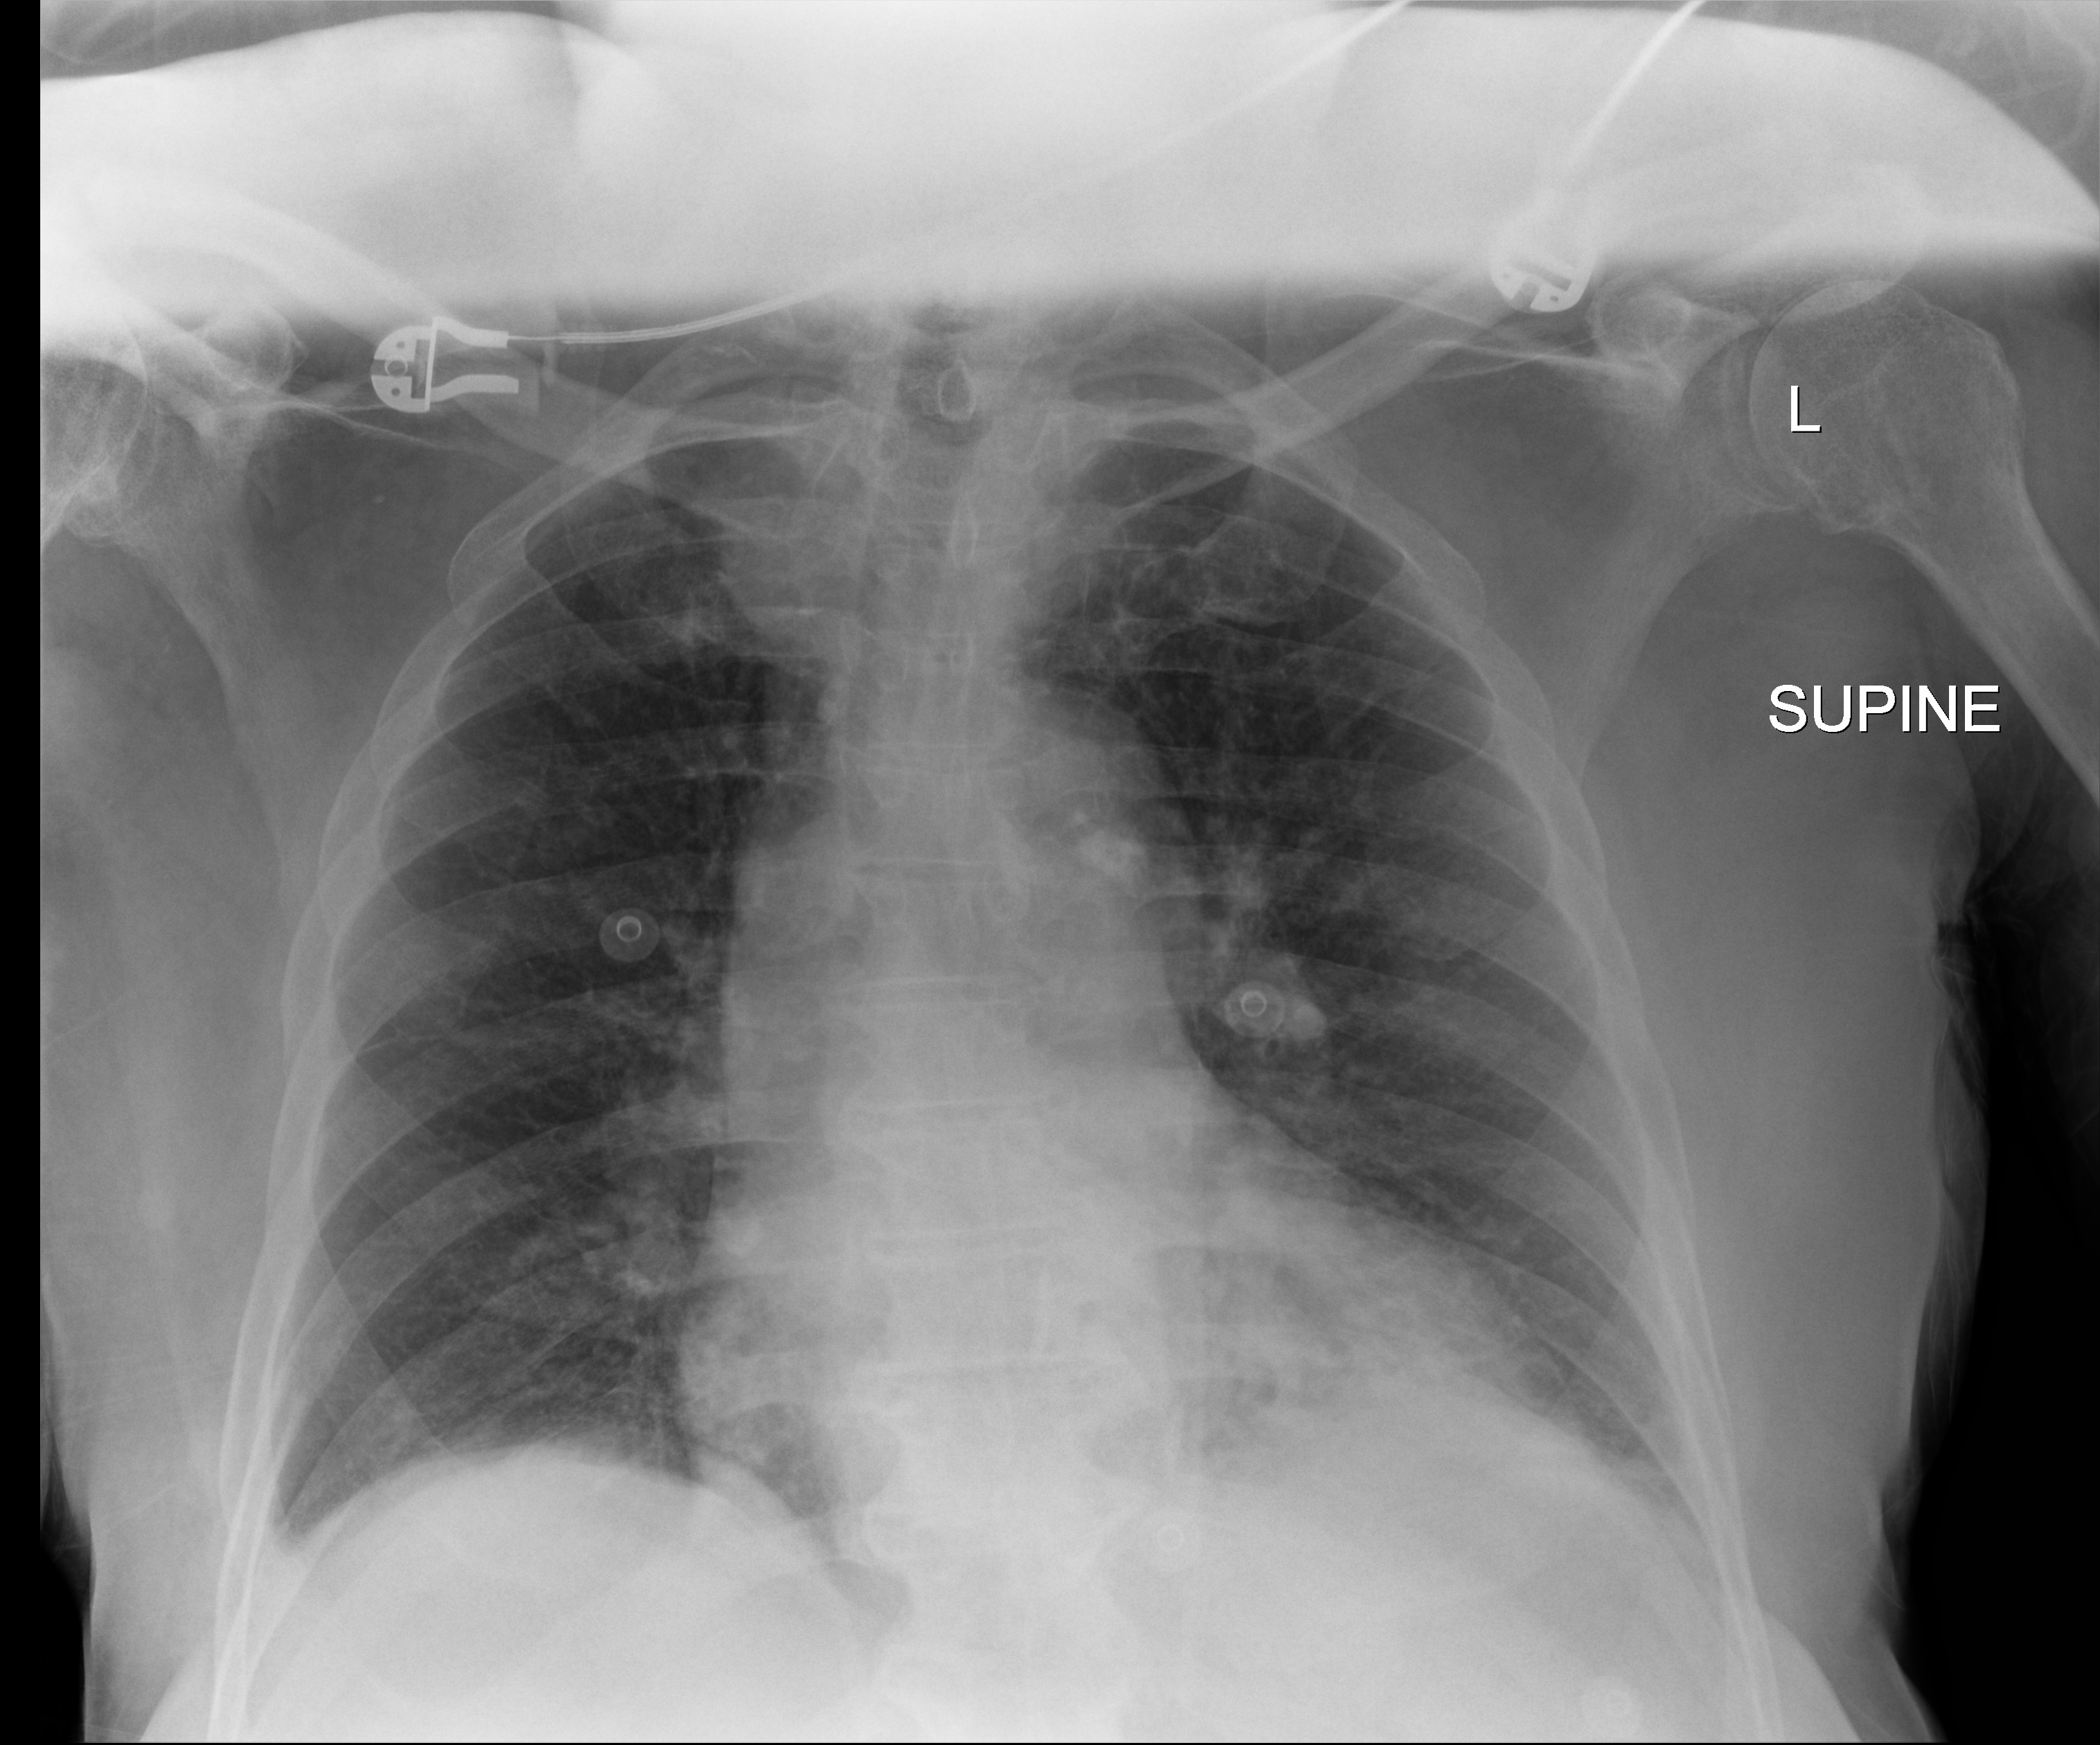
Bedside chest radiograph (digital radiography), anteroposterior (AP) projection. Male patient hospitalised with COVID-19, age 75–90 years.
Hospital-stay facts (about this admission, not read from this image; timing relative to this image not recorded): admitted to intensive care during this hospital stay: no; length of hospital stay: 2 days; mechanically ventilated during this hospital stay: no.